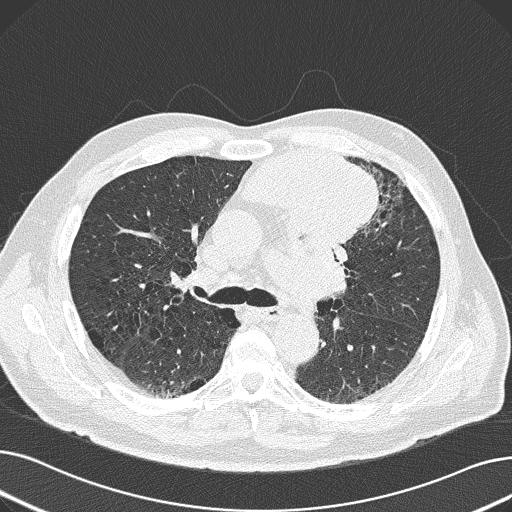
Low-dose screening chest CT, axial slice; baseline annual screen; lung window (W 1500 / L -600 HU); 2 mm slice thickness. Male participant, aged 69 years at enrolment. Former smoker at enrolment.
- Expert-annotated lung lesion, bounding box (x1, y1, x2, y2) in pixels: (233, 137, 383, 251).
- The exam's reader record, not a measurement of the box and not confirmed to be the same lesion: non-calcified nodule or mass ≥4 mm, left upper lobe, 6 × 10 mm, spiculated (stellate) margins, soft tissue attenuation.
- Official screen result: positive, change unspecified: nodule(s) >= 4 mm or enlarging nodule(s), mass(es), or other non-specific abnormalities suspicious for lung cancer.
- Participant outcome: lung cancer diagnosed 20 days after this screen — non-small cell carcinoma, left upper lobe, poorly differentiated (G3), stage IB (AJCC 6th edition), 100 mm at pathology.